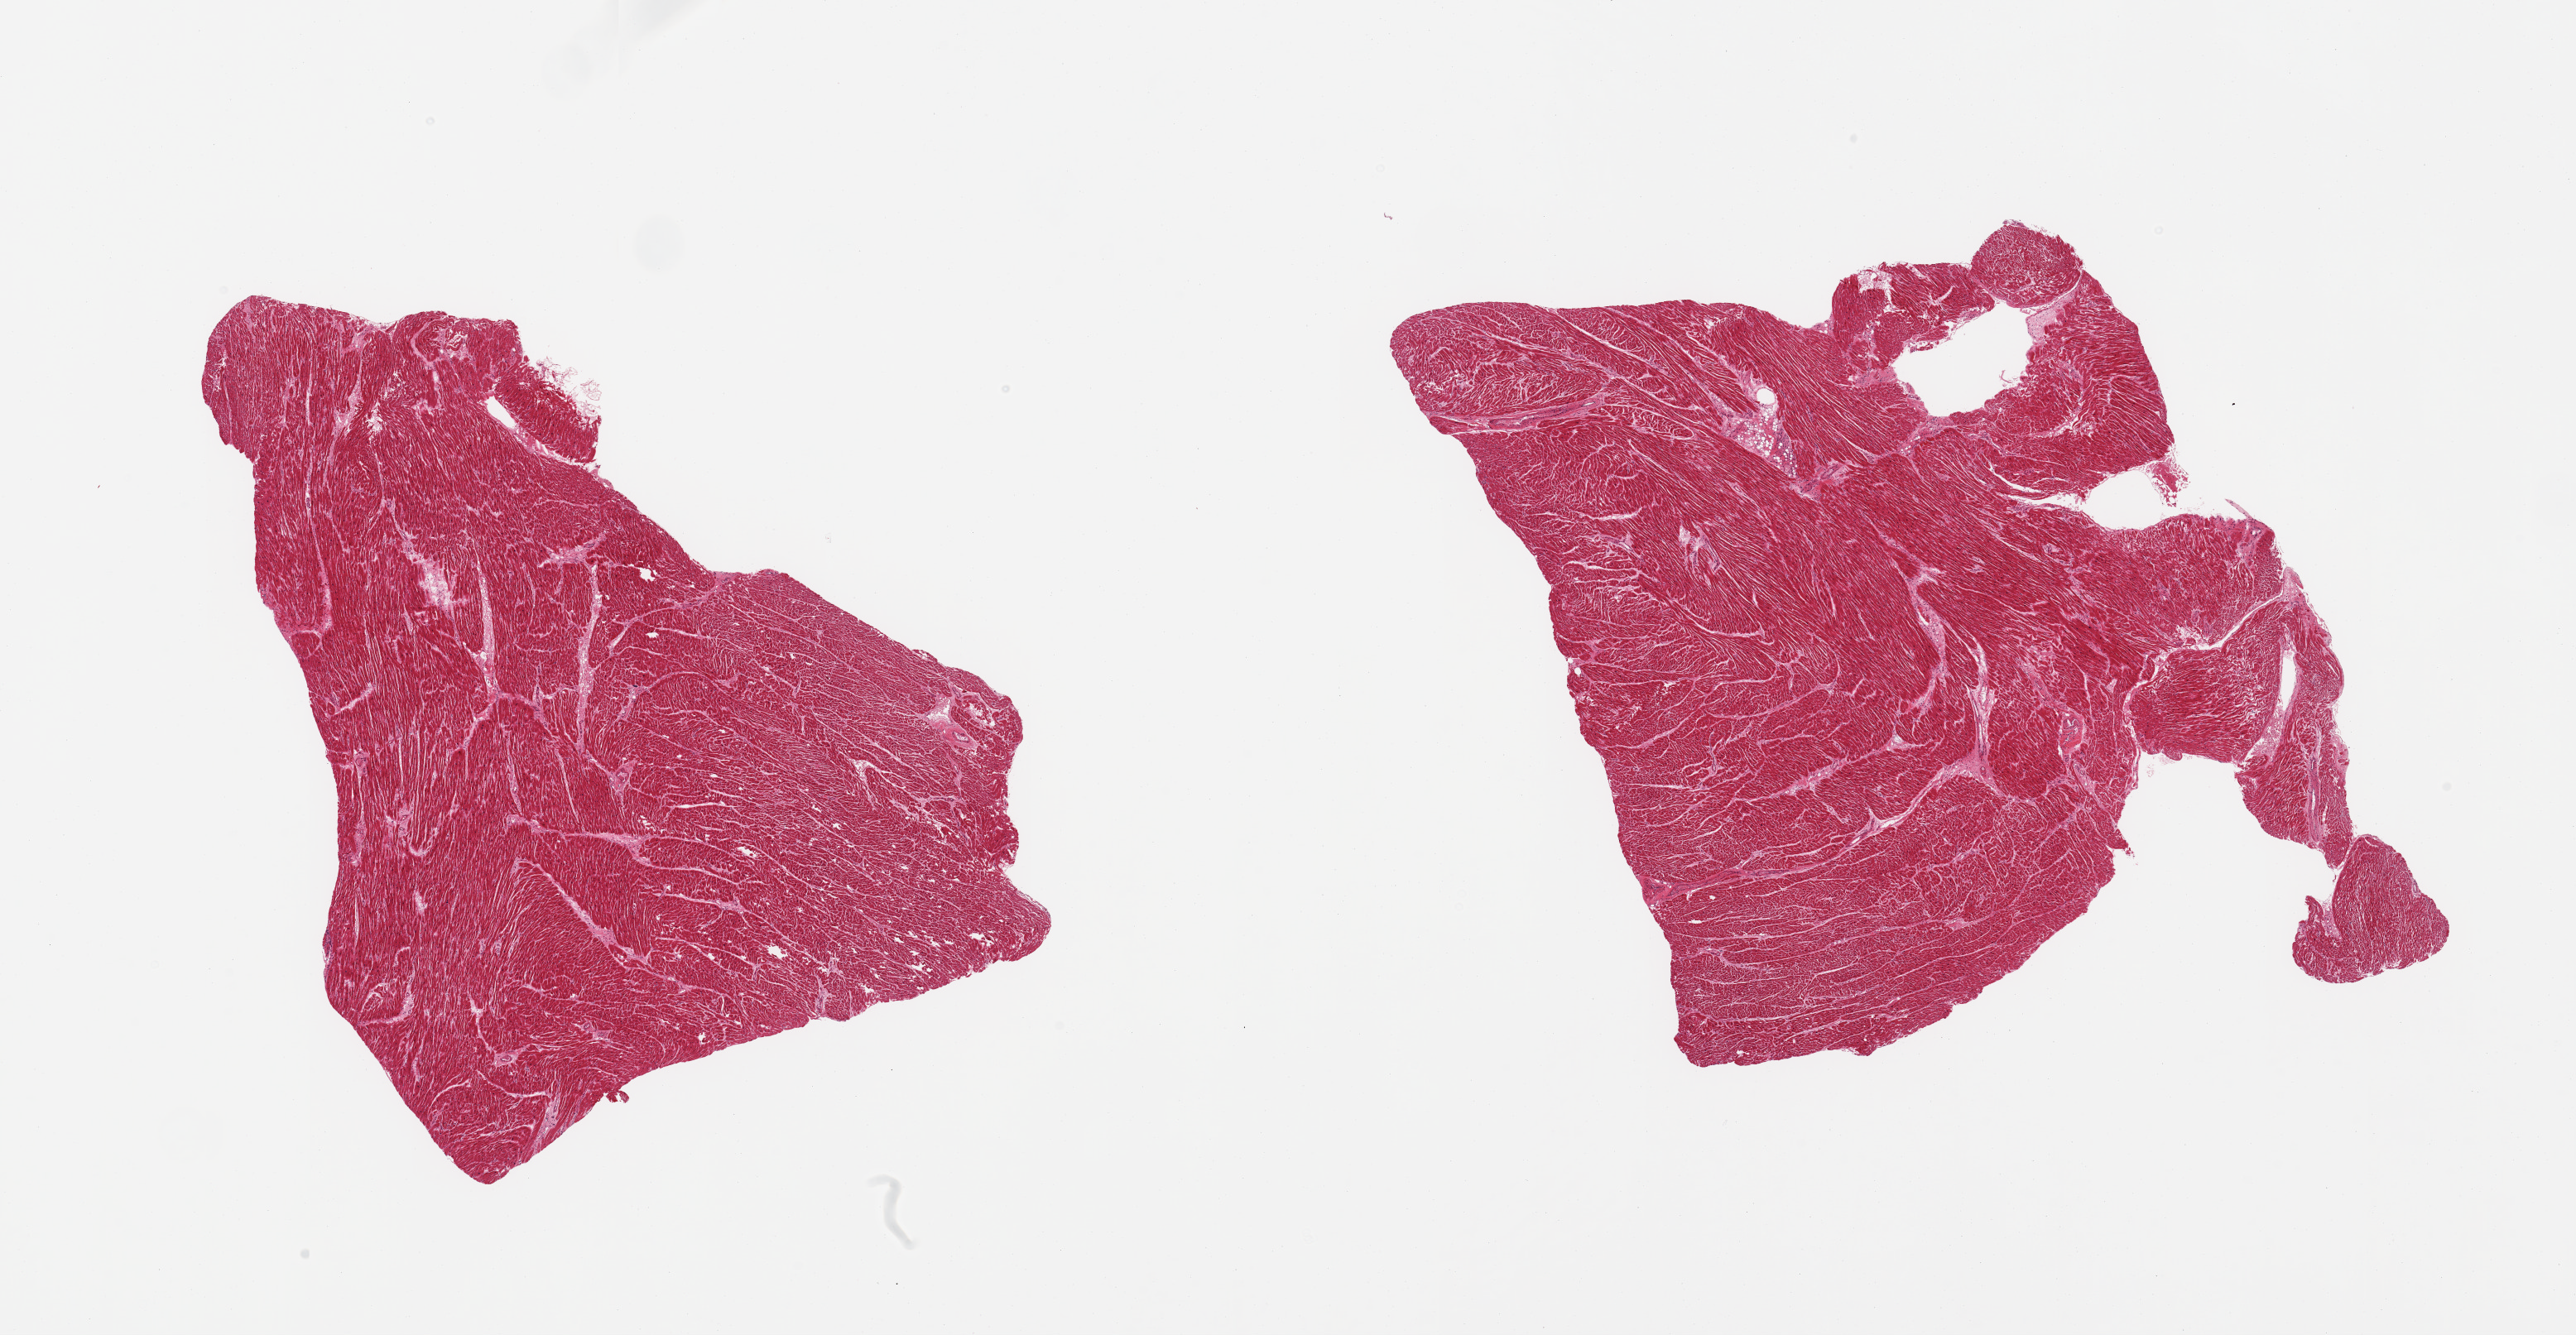
H&E whole-slide image, brightfield, low-resolution overview of the scanned area, about 24.6 x 12.8 mm; PAXgene-fixed paraffin-embedded (PFPE) section; sampled site (target tissue): heart; donor tissue sample. Donor: male.
• review note (as recorded): 2 pieces